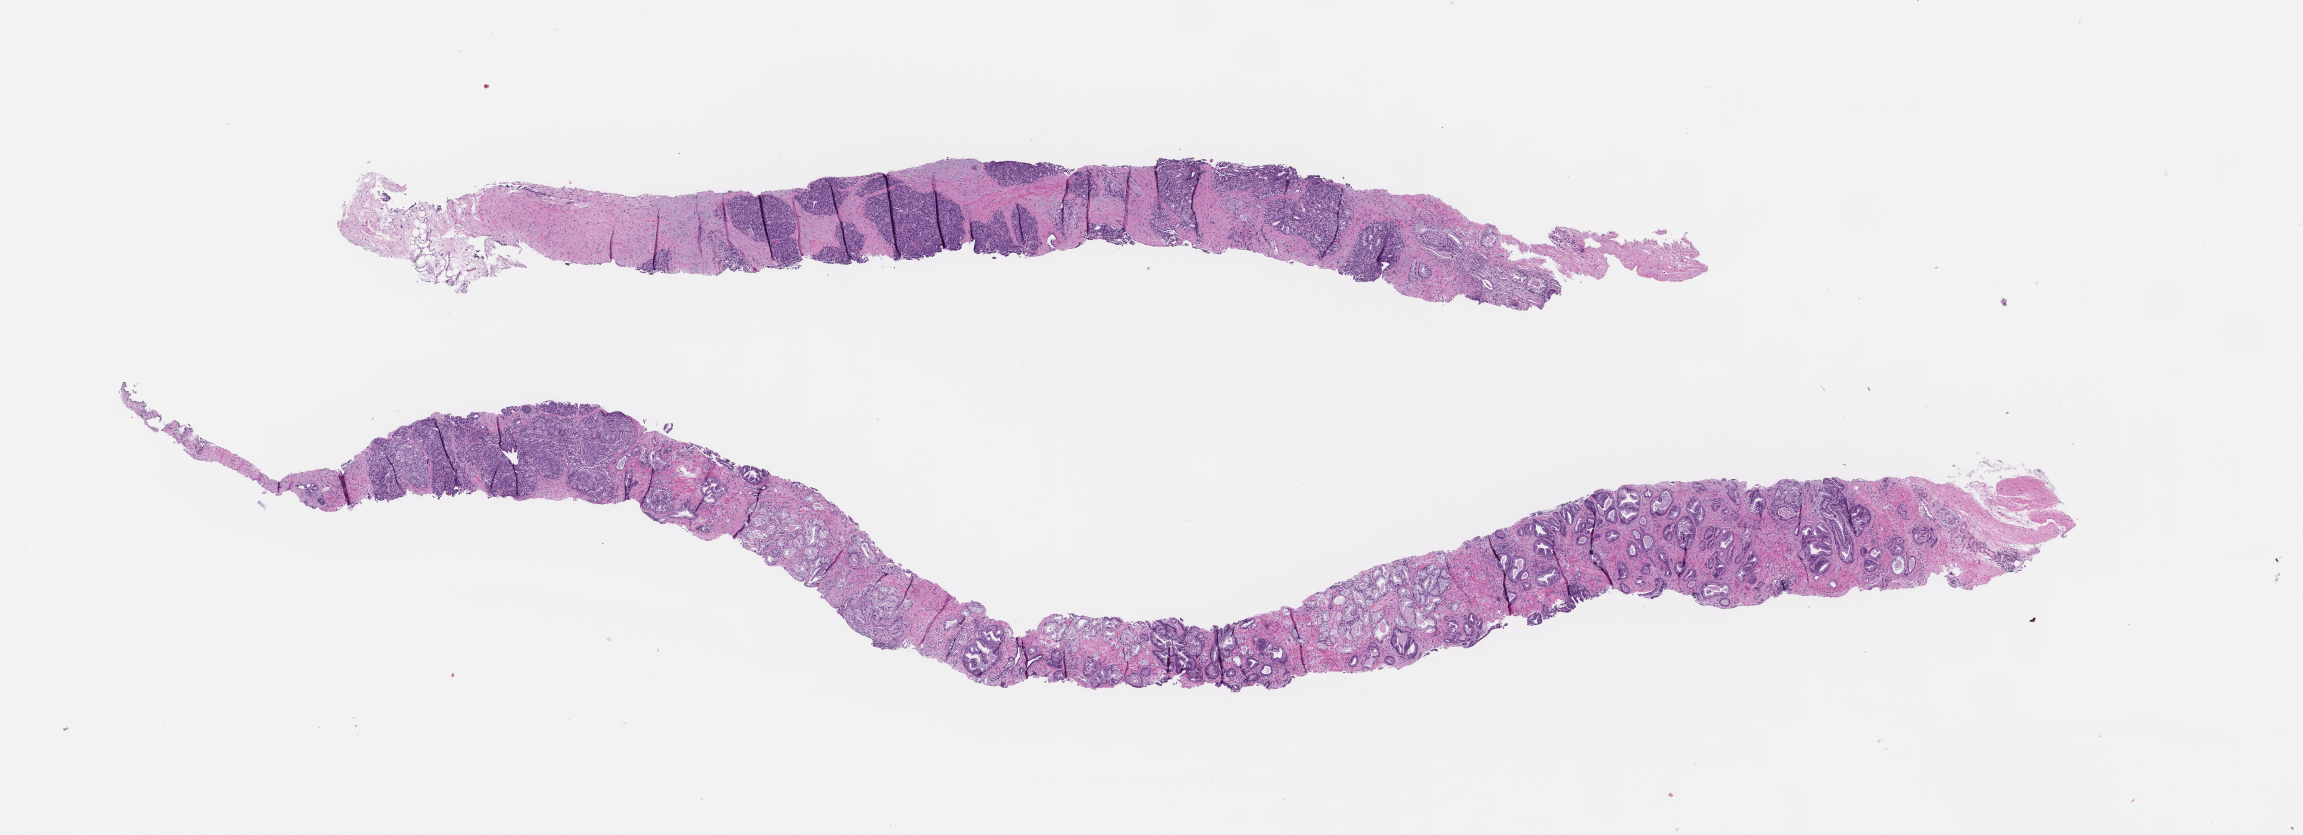
Whole-slide image, hematoxylin and eosin (H&E) stain — low-resolution overview of the scanned area, about 18.6 x 6.7 mm, formalin-fixed, paraffin-embedded (FFPE) tissue. Male patient.
• this section: metastasis (sampled organ not recorded)
• primary diagnosis of the patient: Prostate Carcinoma